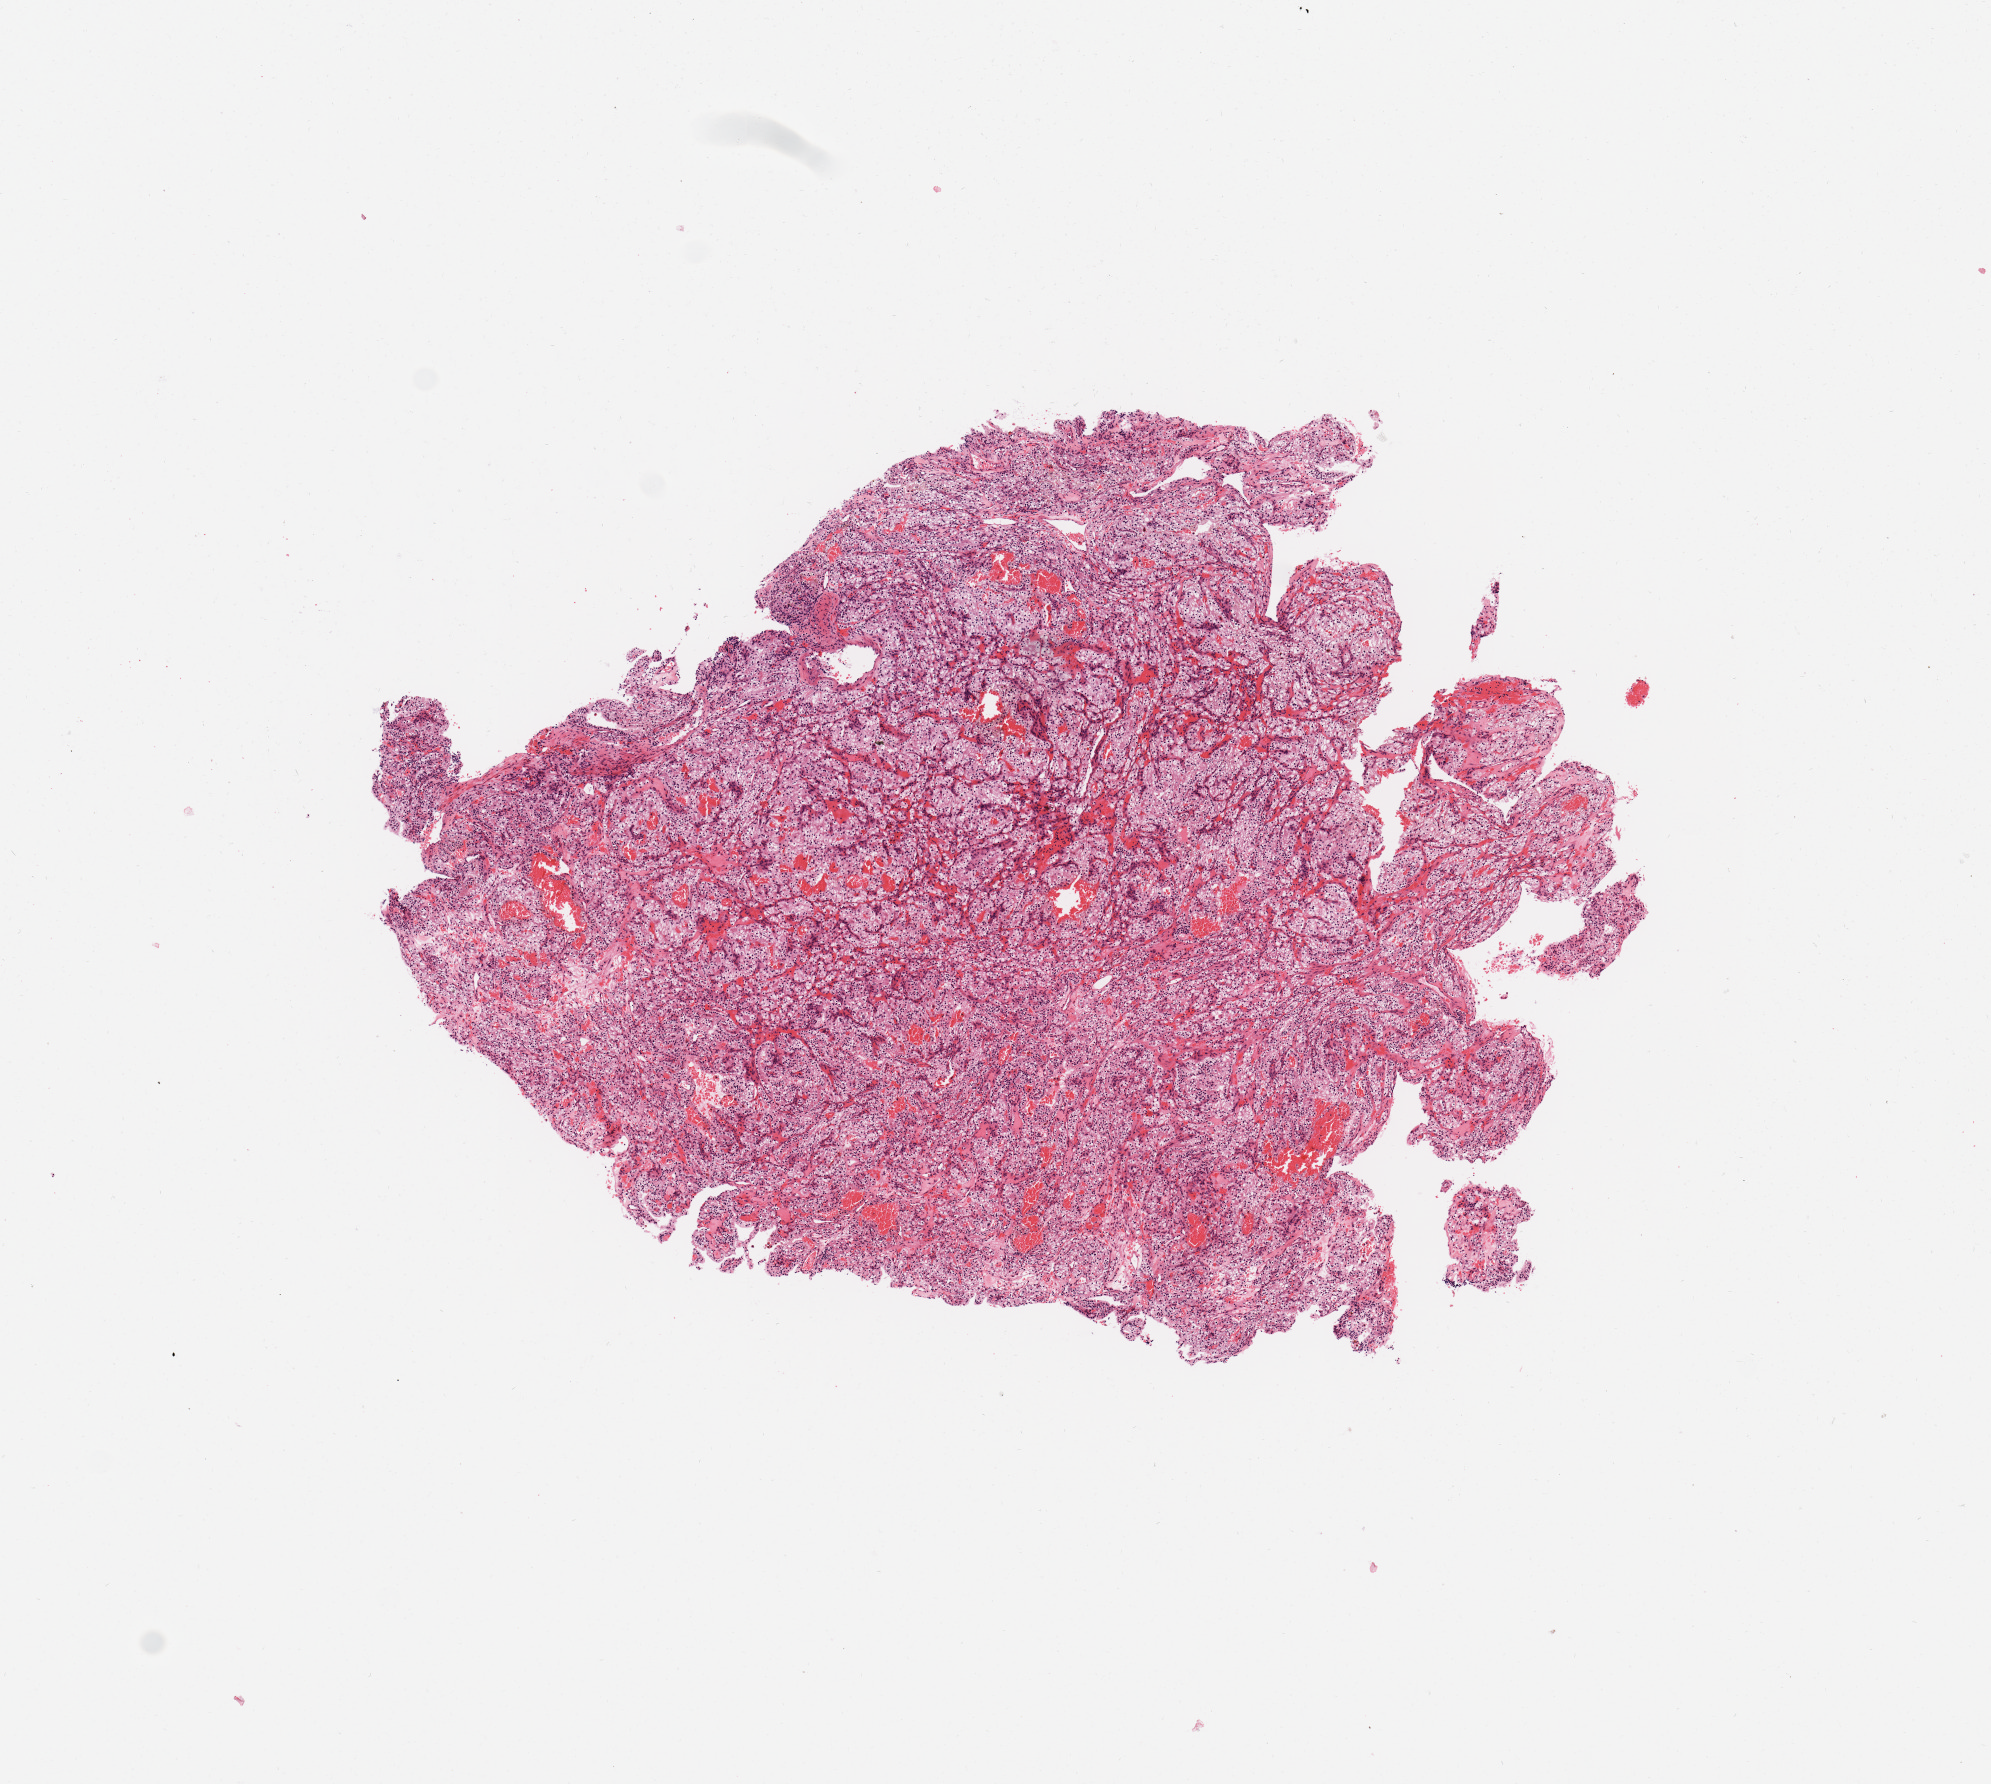
H&E-stained whole-slide image, low-resolution overview of the scanned area, about 7.9 x 7.1 mm (slide scanned at 20x). Tumour tissue sample, sampled site: kidney. Male, 46 y/o.
Diagnosis: Renal cell carcinoma, NOS.